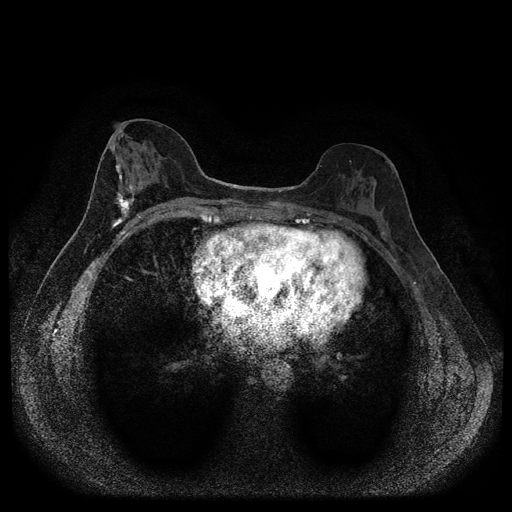
Breast MRI (dynamic contrast-enhanced, multi-phase), one axial slice; position 46 of 116 along the scan axis; dynamic contrast-enhanced series, time point 2 of 5 at this slice position (early post-contrast); 1.5 T; TE 2.7 ms, TR 5.4 ms; 2 mm slice thickness; 512 × 512 image matrix. Female patient, age 49 years.
Outlined on this slice (semi-automatically segmented with operator editing):
- breast lesion (labelled 'tumour' in the annotation; benign lesions carry a separate 'benign' label): box from (x=114, y=158) to (x=139, y=221) px